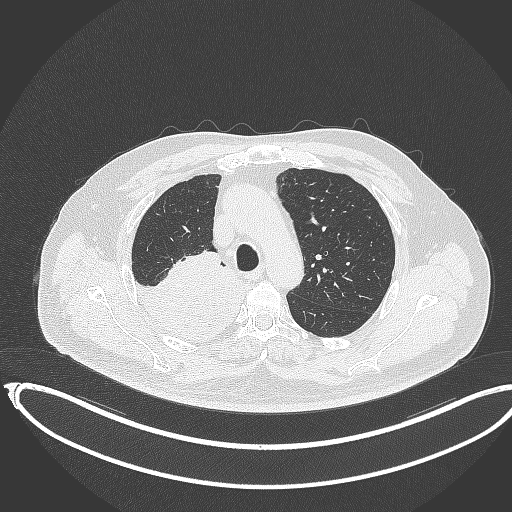
Chest CT, one axial slice. Position 265 of 403 along the scan axis. Reconstruction kernel B70f. 120 kVp. Lung window (W 1500 / L -600 HU). 1 mm slice thickness. 512 × 512 image matrix, field of view 436 × 436 mm. Patient: male, 68 years. Case-level facts recorded for this patient, not image findings: clinical TNM (as recorded): T2a N0 M0.
Structures marked on this image (bounding box drawn by a radiologist):
- lung tumour (recorded histology: adenocarcinoma): bounding box (x1, y1, x2, y2) in pixels: (122, 257, 247, 344)